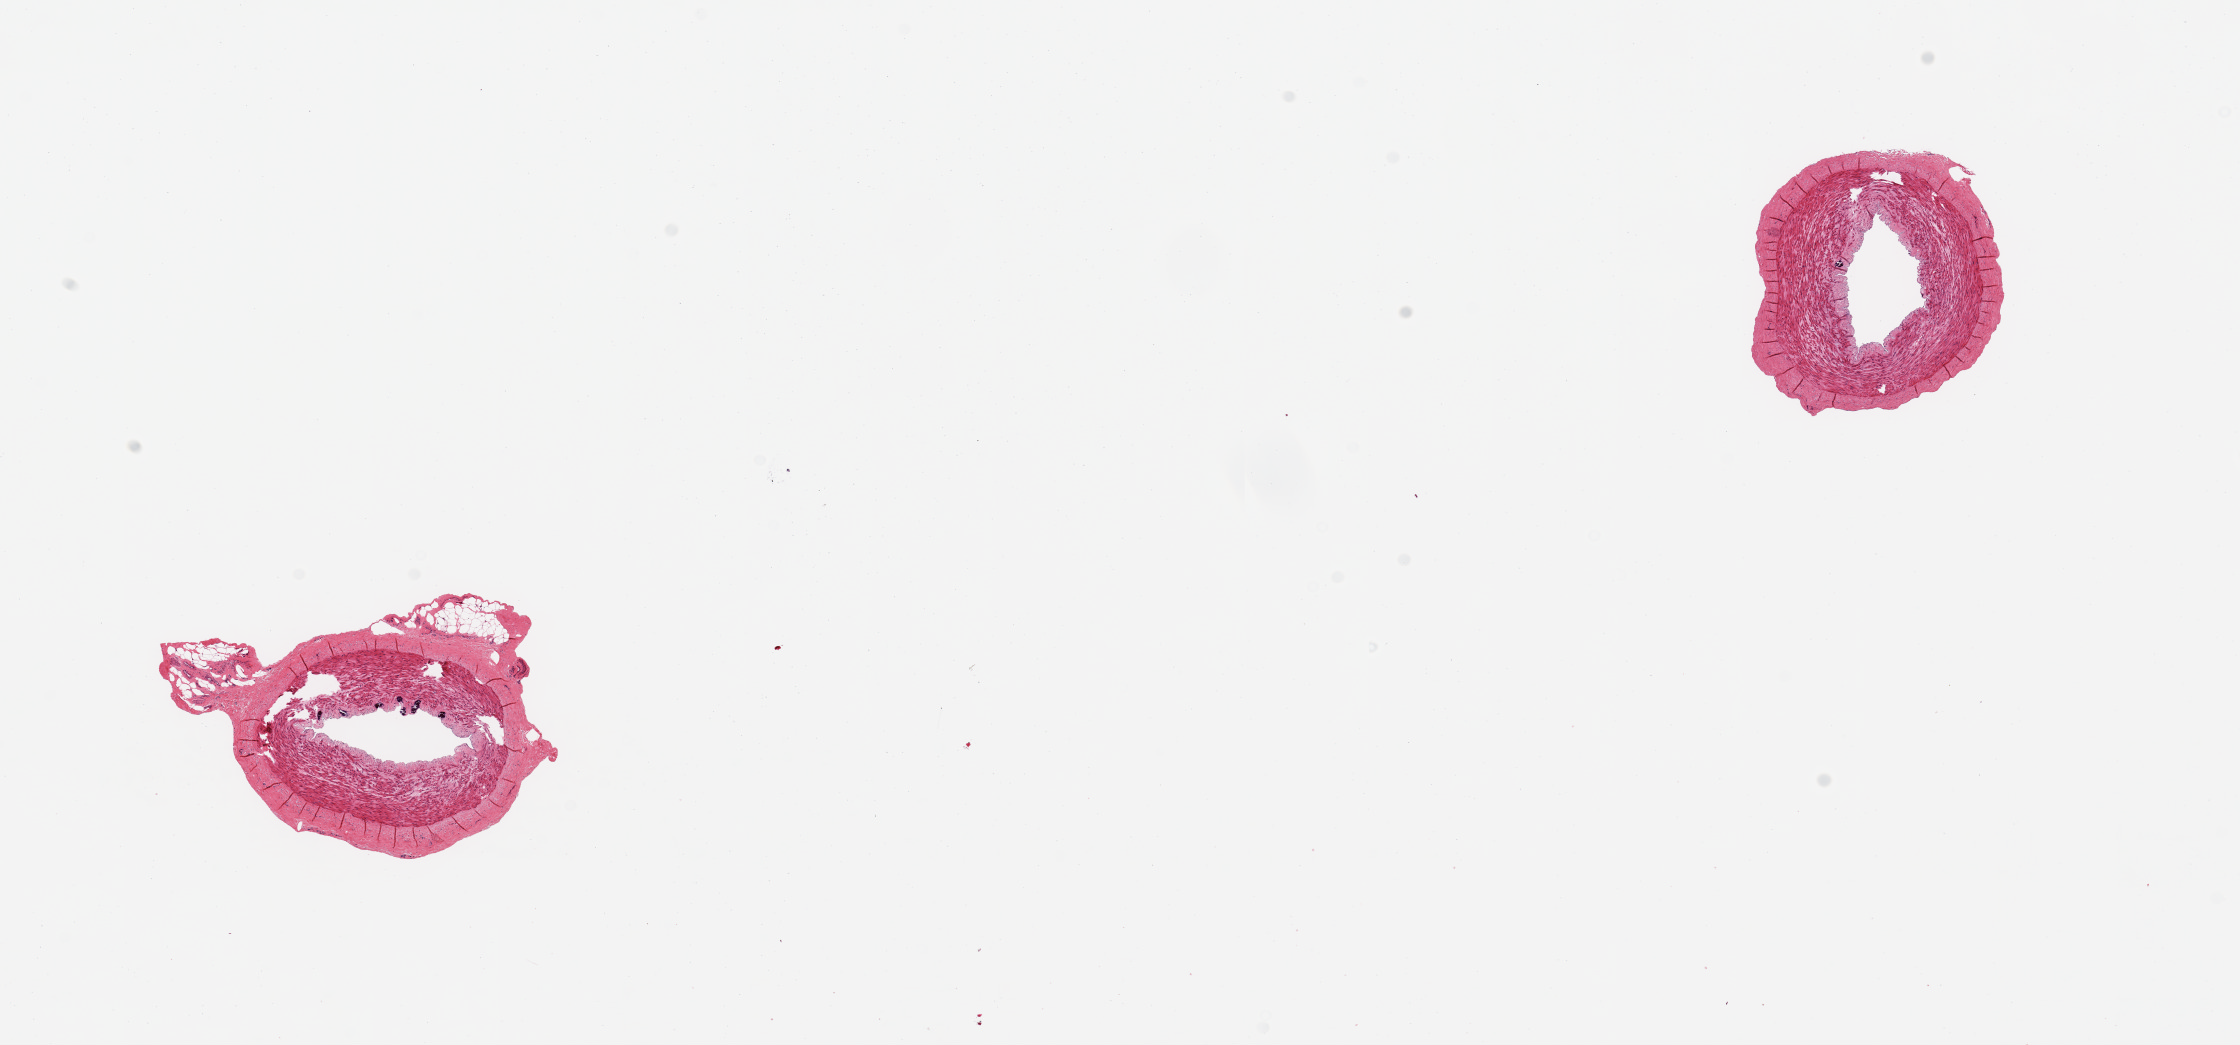
Digitized haematoxylin and eosin-stained section, whole scanned area (about 17.7 x 8.3 mm) shown as a low-resolution overview, PAXgene-fixed paraffin-embedded (PFPE) section, section of tibial artery (target tissue), tissue donor sample. Donor: male.
Reviewer comment on this tissue sample: 2 pieces of 2 muscular arteries about 2mm in diameter; calcified deposits in intima; 10% adherent fat in one piece.